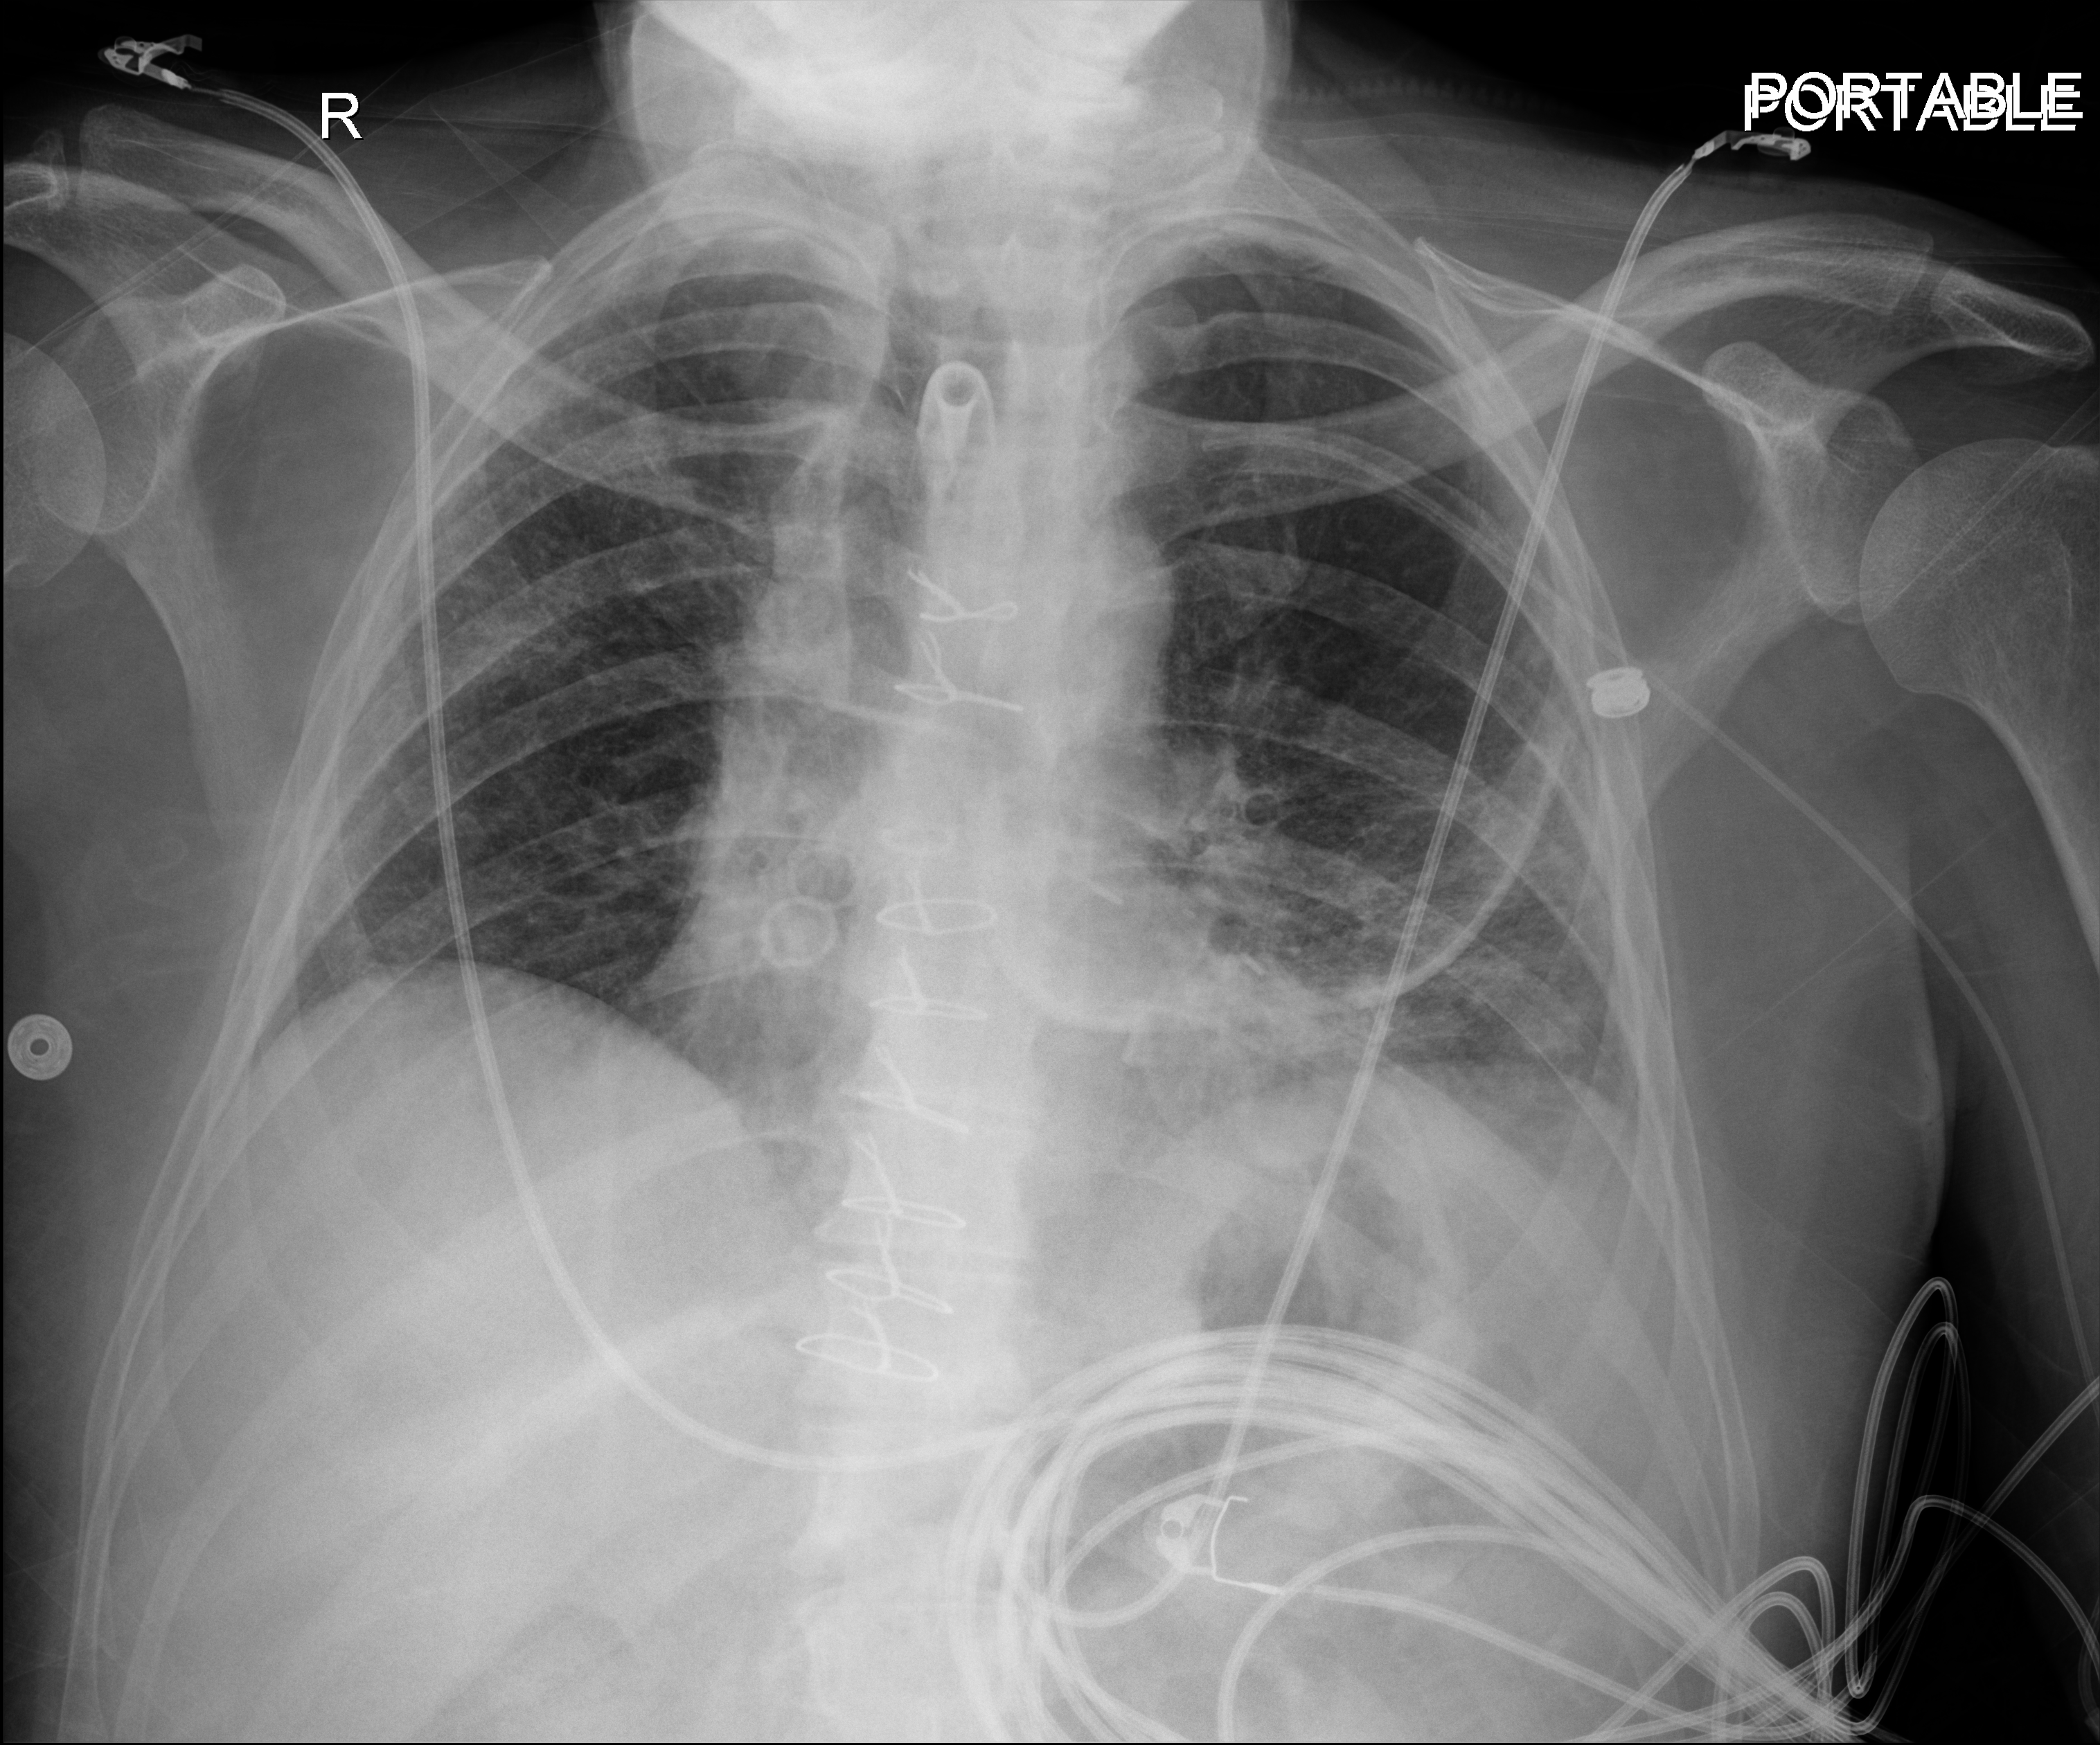
Bedside chest radiograph (digital radiography), anteroposterior (AP) projection. Male patient hospitalised with COVID-19, age 18–59 years.
Admission-level facts for this patient (not findings on this image; timing relative to this image not recorded):
- chronic kidney disease (admission record): no
- mechanically ventilated during this hospital stay: yes
- admitted to intensive care during this hospital stay: yes